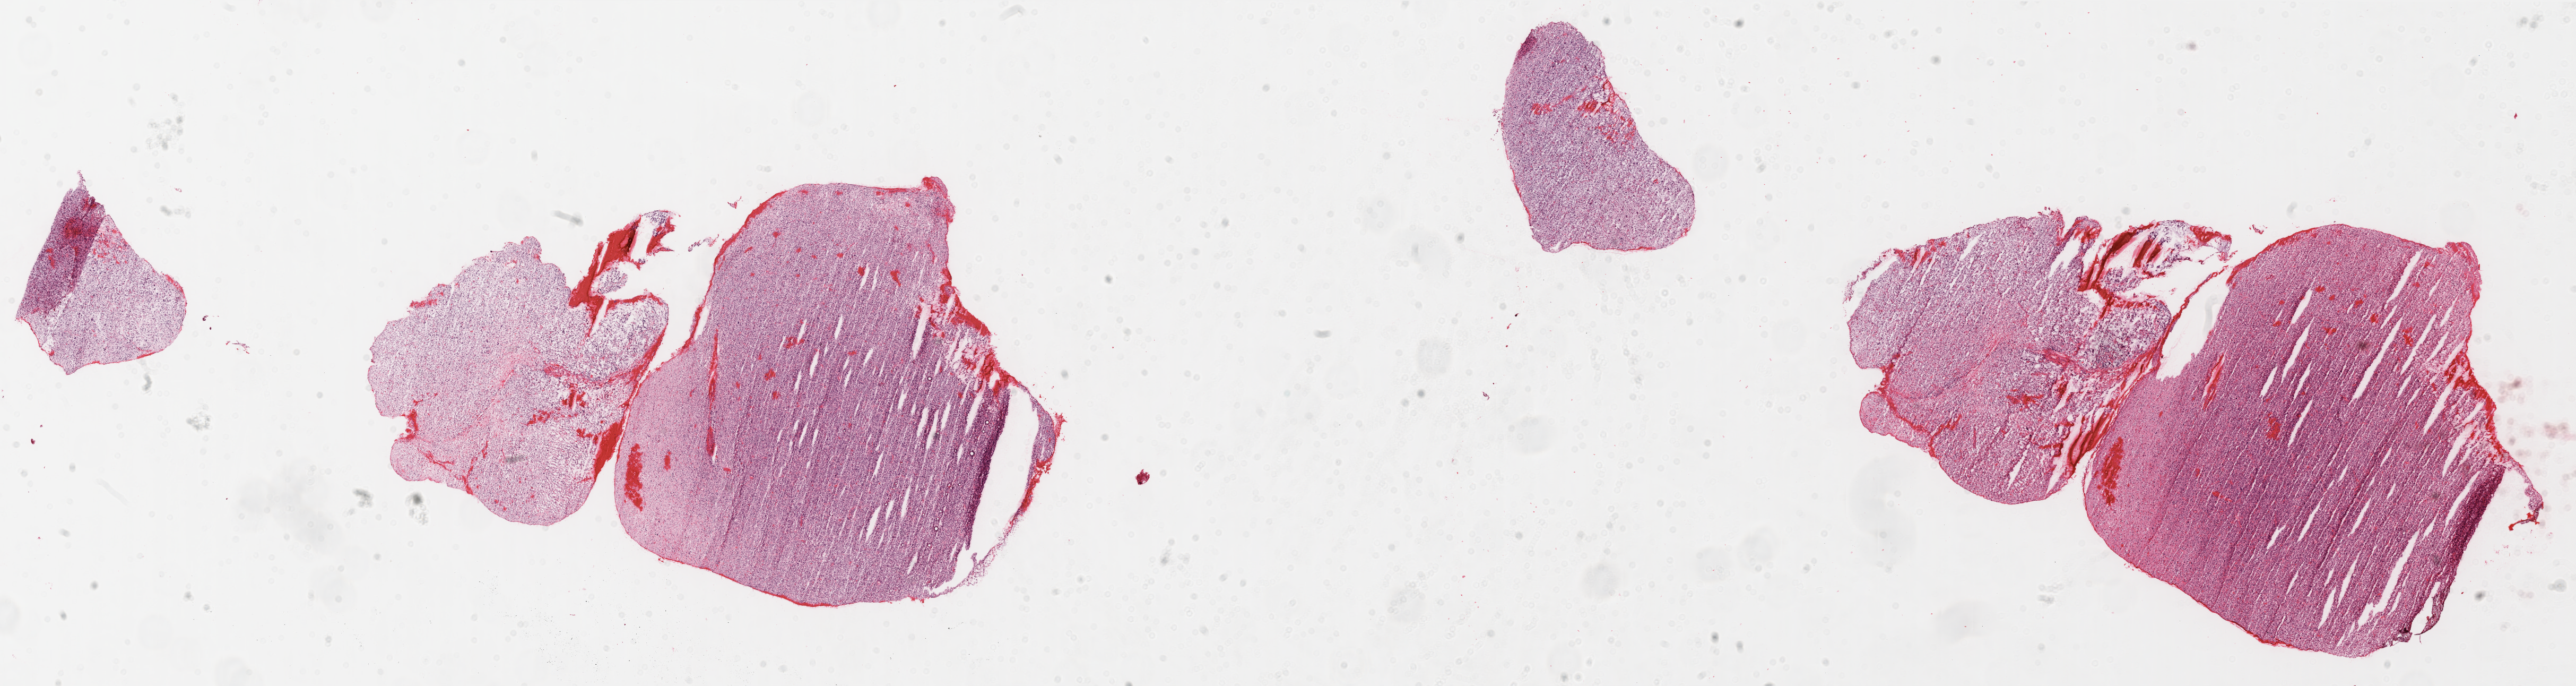
Hematoxylin and eosin (H&E) stained whole-slide image — low-resolution overview of the scanned area, about 39.0 x 10.4 mm (acquisition: 20x scan). FFPE section. Primary tumour sample from the brain. Patient: male, age at initial diagnosis 25 years.
Pathologic diagnosis: Glioblastoma.